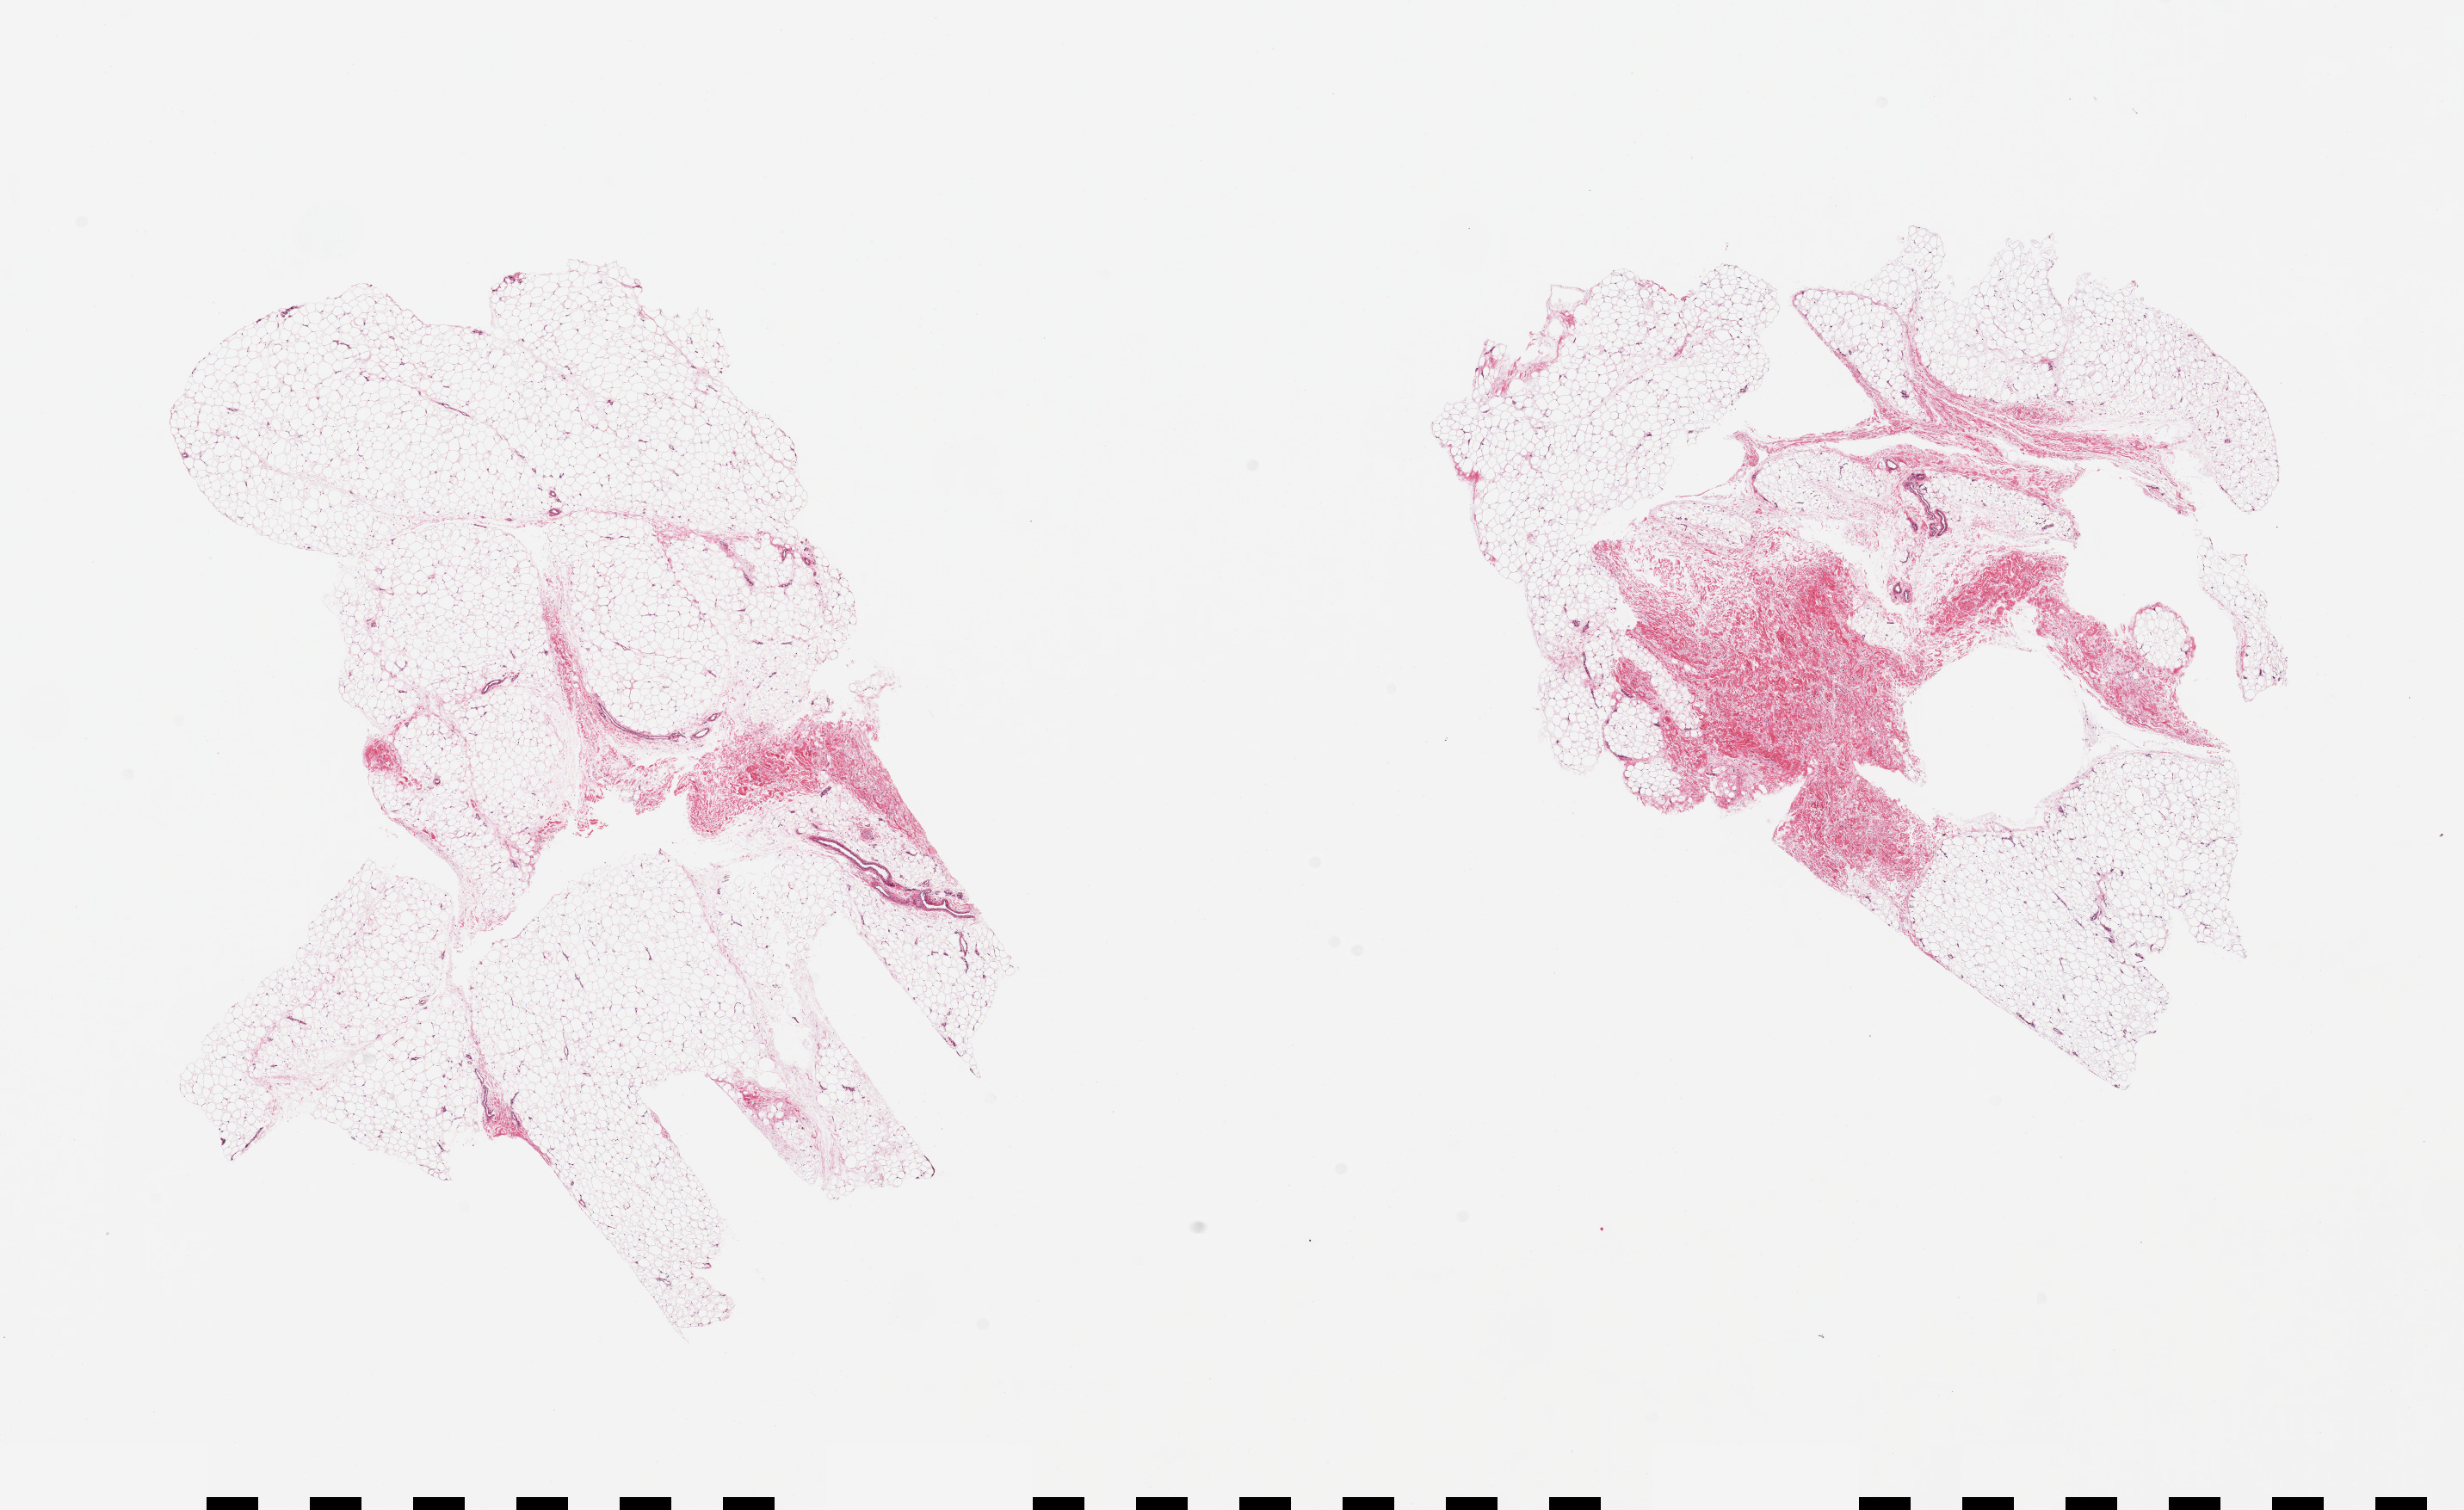
Whole-slide image, H&E stain — a low-resolution overview of the entire scanned area, about 22.6 x 13.9 mm. PAXgene-fixed, paraffin-embedded tissue. Sampled site (target tissue): adipose tissue. Donor tissue sample. Donor sex: female.
Review note (as recorded): 2 pieces; 20% fibrous content in 1, 5% in other.